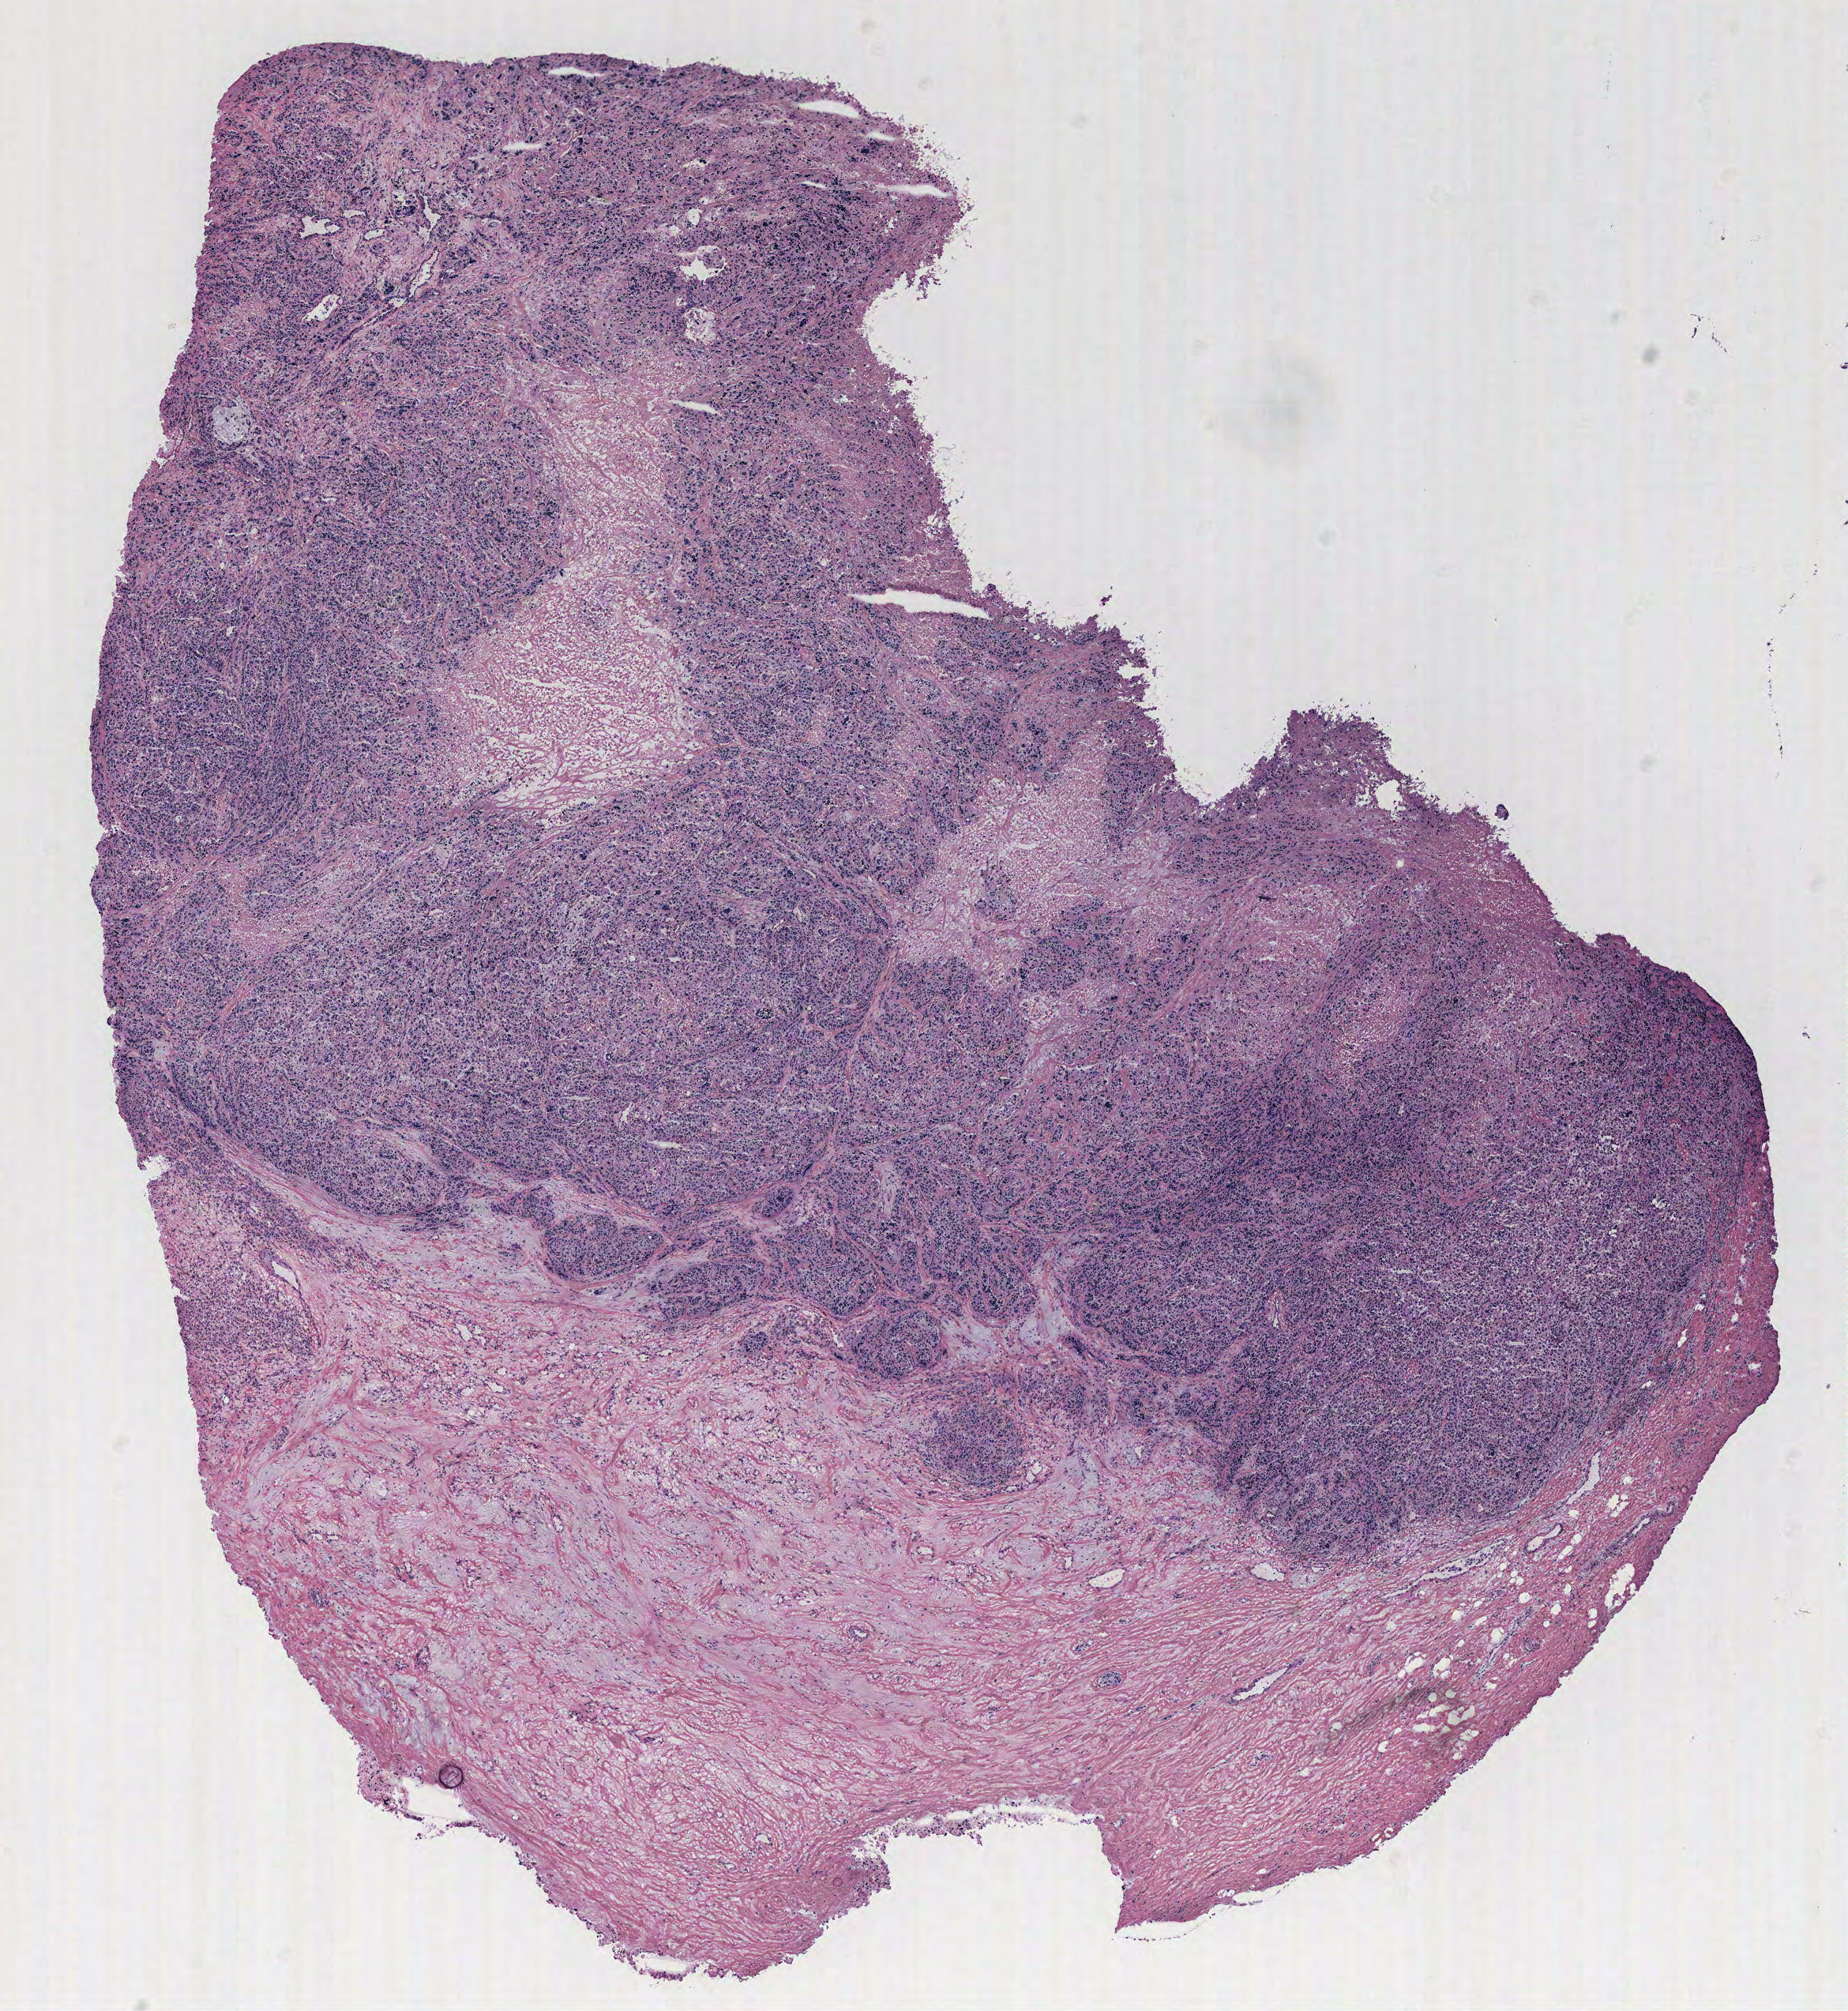
Digitized H&E-stained tissue section (whole slide), whole scanned area (about 9.4 x 10.2 mm) shown as a low-resolution overview; breast, tissue type not recorded. Female, 65 y/o.
* patient diagnosis: Infiltrating duct carcinoma, NOS